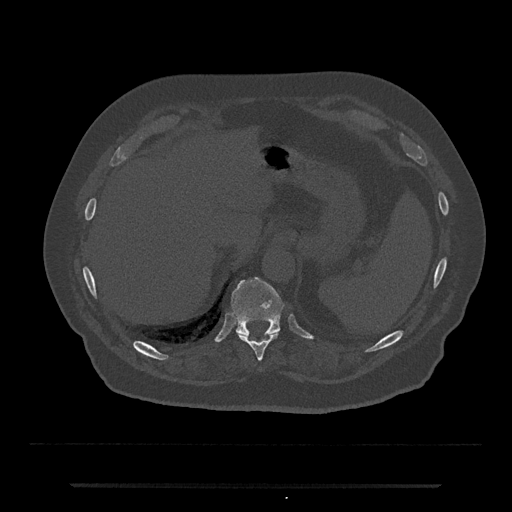
CT including the spine, one axial slice. Slice 679 of 797 in the series (ordered by position). Bone window (W 1800 / L 400 HU). 512 × 512 image matrix, field of view 434 × 434 mm. Patient: male, 80 years. From the clinical record (not read from this slice): primary cancer: prostate; vertebrae with lytic lesions (as recorded): L1, T11.
Outlined on this slice (semi-automatic segmentation, software-assisted and operator-edited):
- T10 vertebra: bounding box (x1, y1, x2, y2) in pixels: (238, 332, 278, 361)
- T11 vertebra: (231, 277, 284, 336)